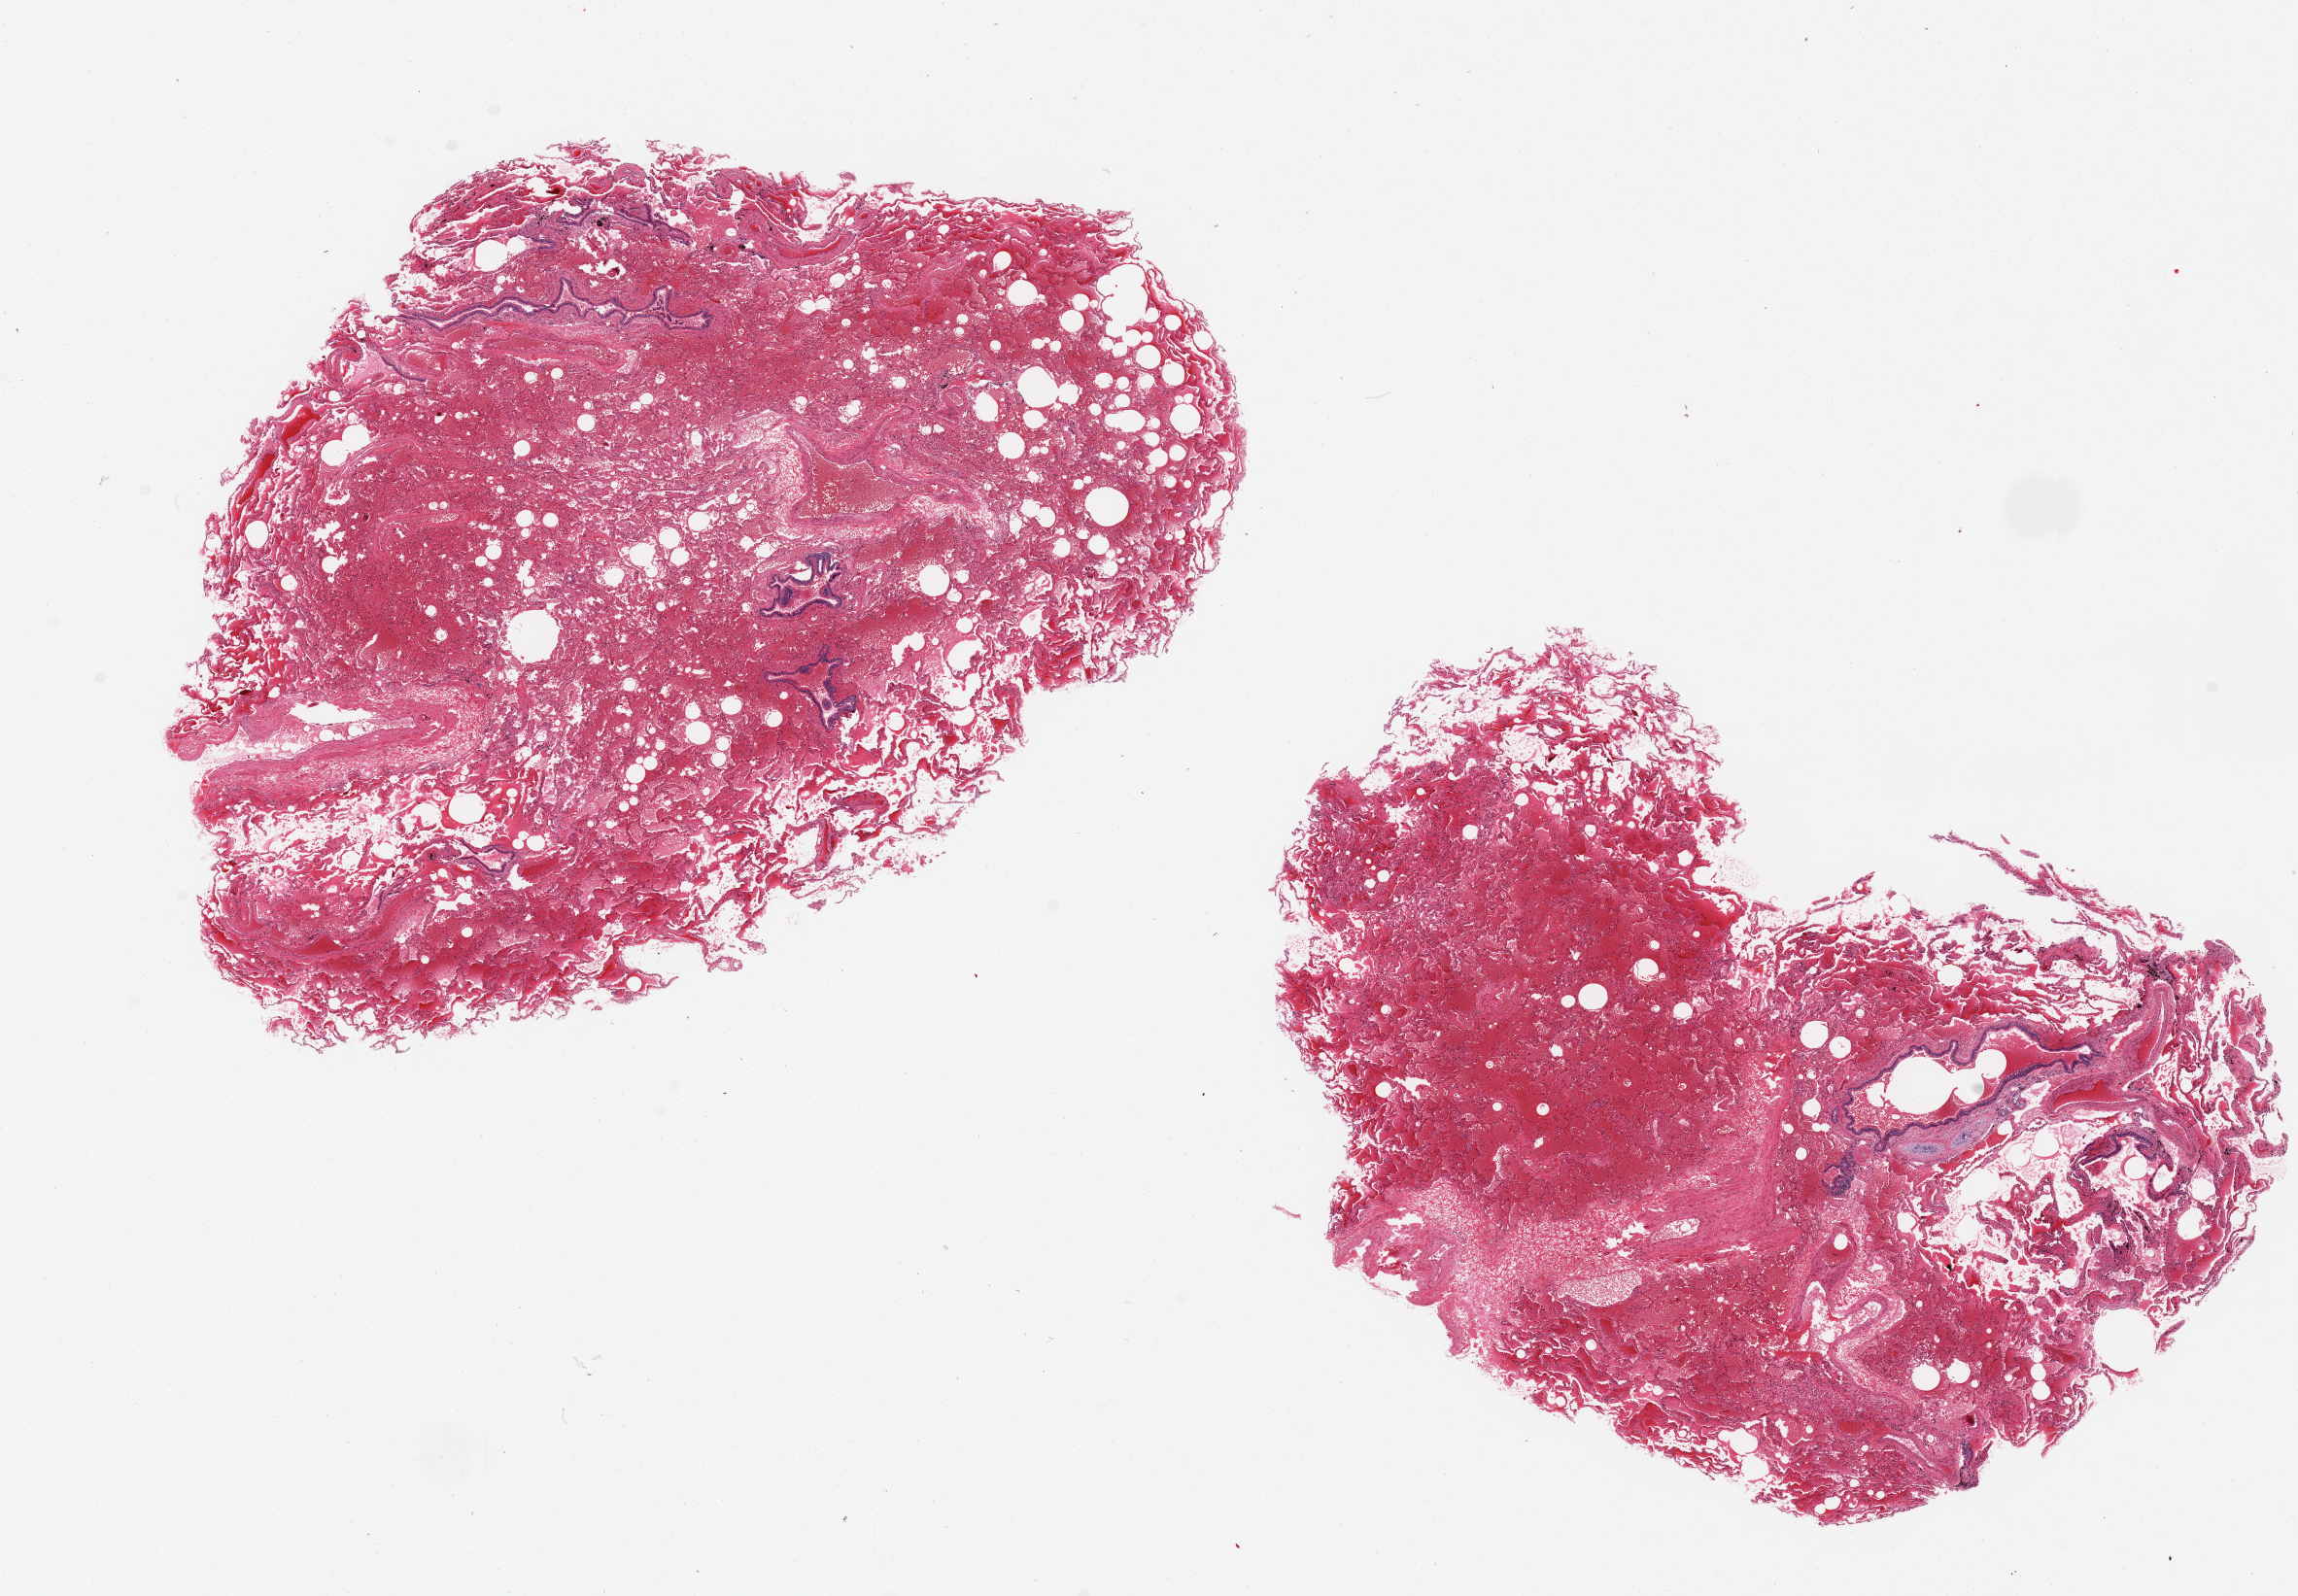
Digitized hematoxylin and eosin (H&E)-stained section — shown as a low-resolution overview of the whole scanned area (about 18.7 x 13.0 mm), PAXgene-fixed, paraffin-embedded tissue, sampled site (target tissue): lung, tissue donor sample. Donor sex: female.
* pathologist's review note for this sample: 2 pieces, 9x6 & 8x5 mm; extensive recent hemorrhage